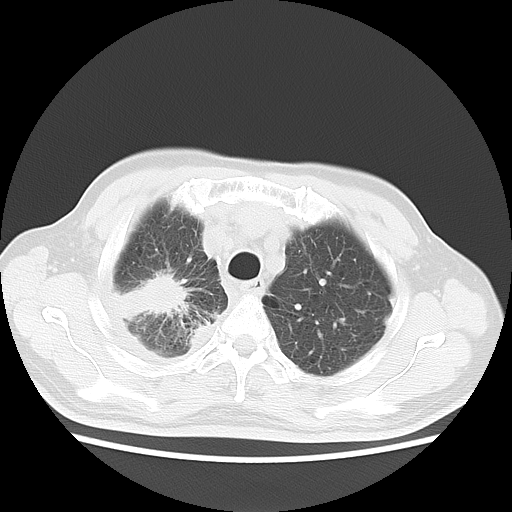
Chest CT, one axial slice; slice 14 of 16 in the series (ordered by position); reconstruction kernel LUNG; 120 kVp; lung window (W 1500 / L -600 HU); 5 mm slice thickness; 512 × 512 image matrix. Male patient, age 75 years. From the clinical record (not read from this slice): clinical TNM (as recorded): T1c N1 M1.
Outlined on this slice (bounding box drawn by a radiologist):
- lung tumour (recorded histology: adenocarcinoma): bounding box <108,266,193,330> (left, top, right, bottom; pixels)